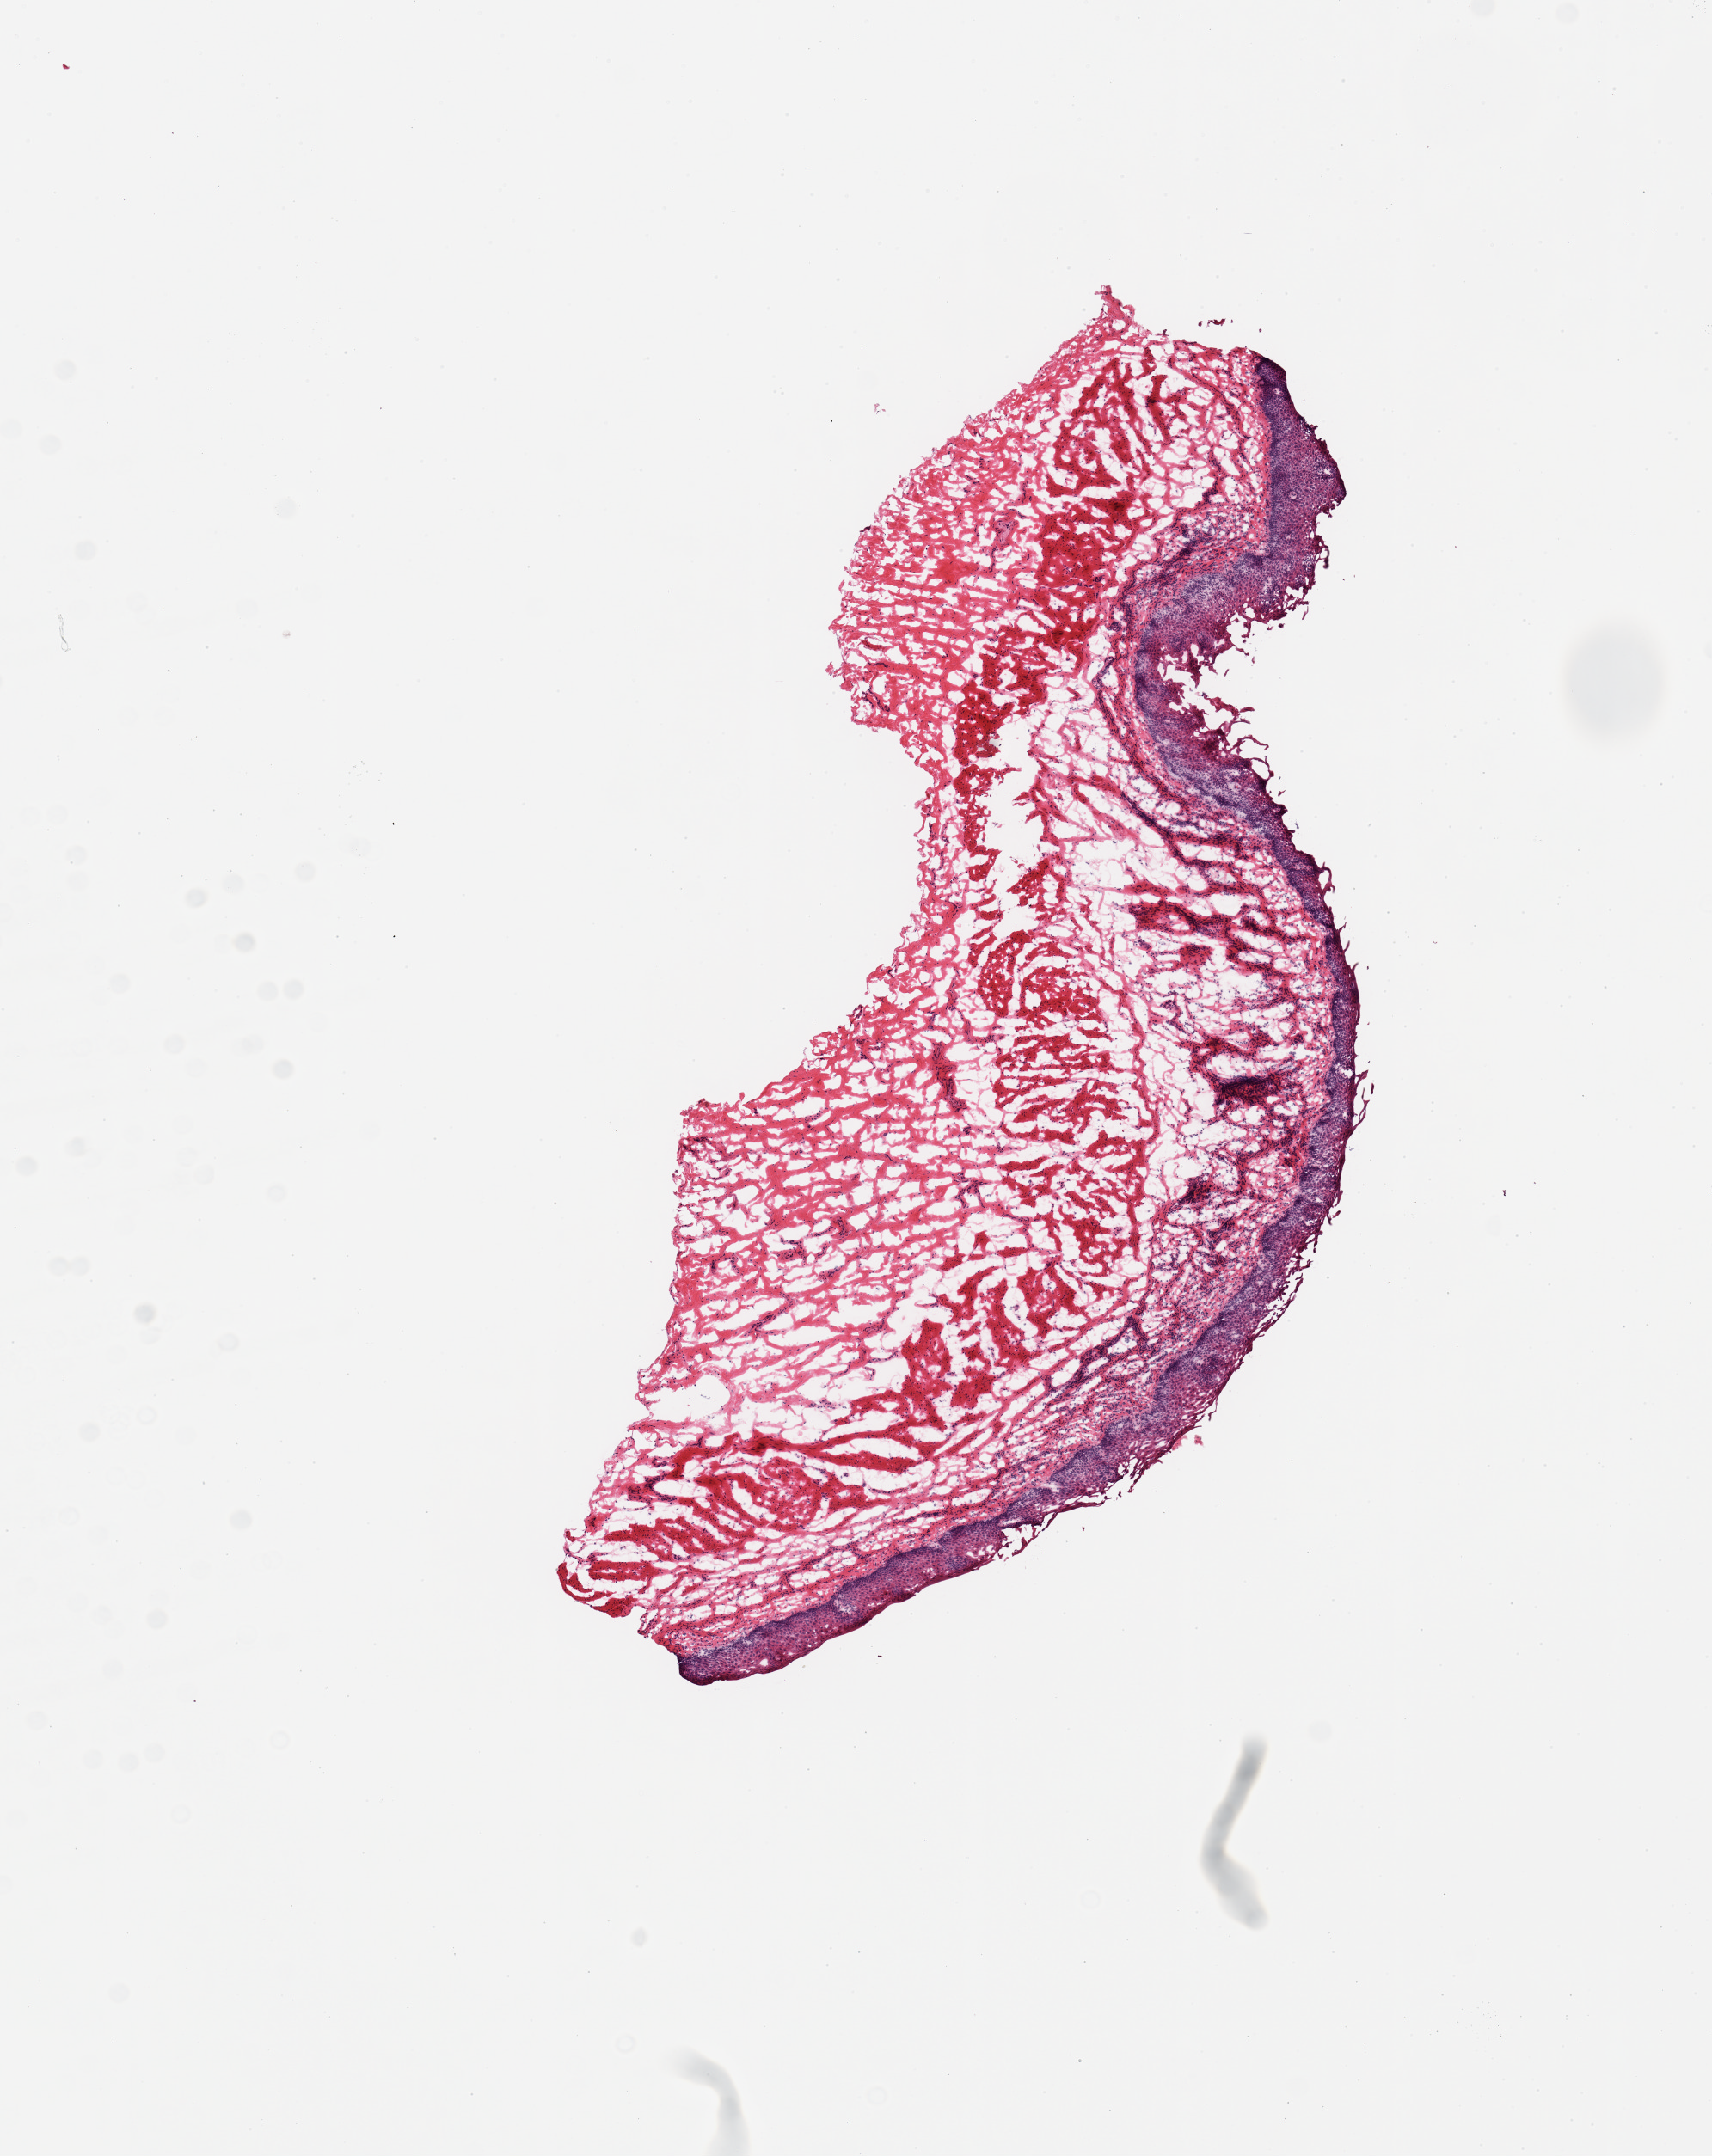
Hematoxylin and eosin (H&E) whole-slide image — low-resolution overview of the scanned area, about 7.9 x 9.9 mm (acquisition: 20x scan). Donor: female.
Specimen: frozen section; section of esophageal mucous membrane (target tissue); donor tissue sample.